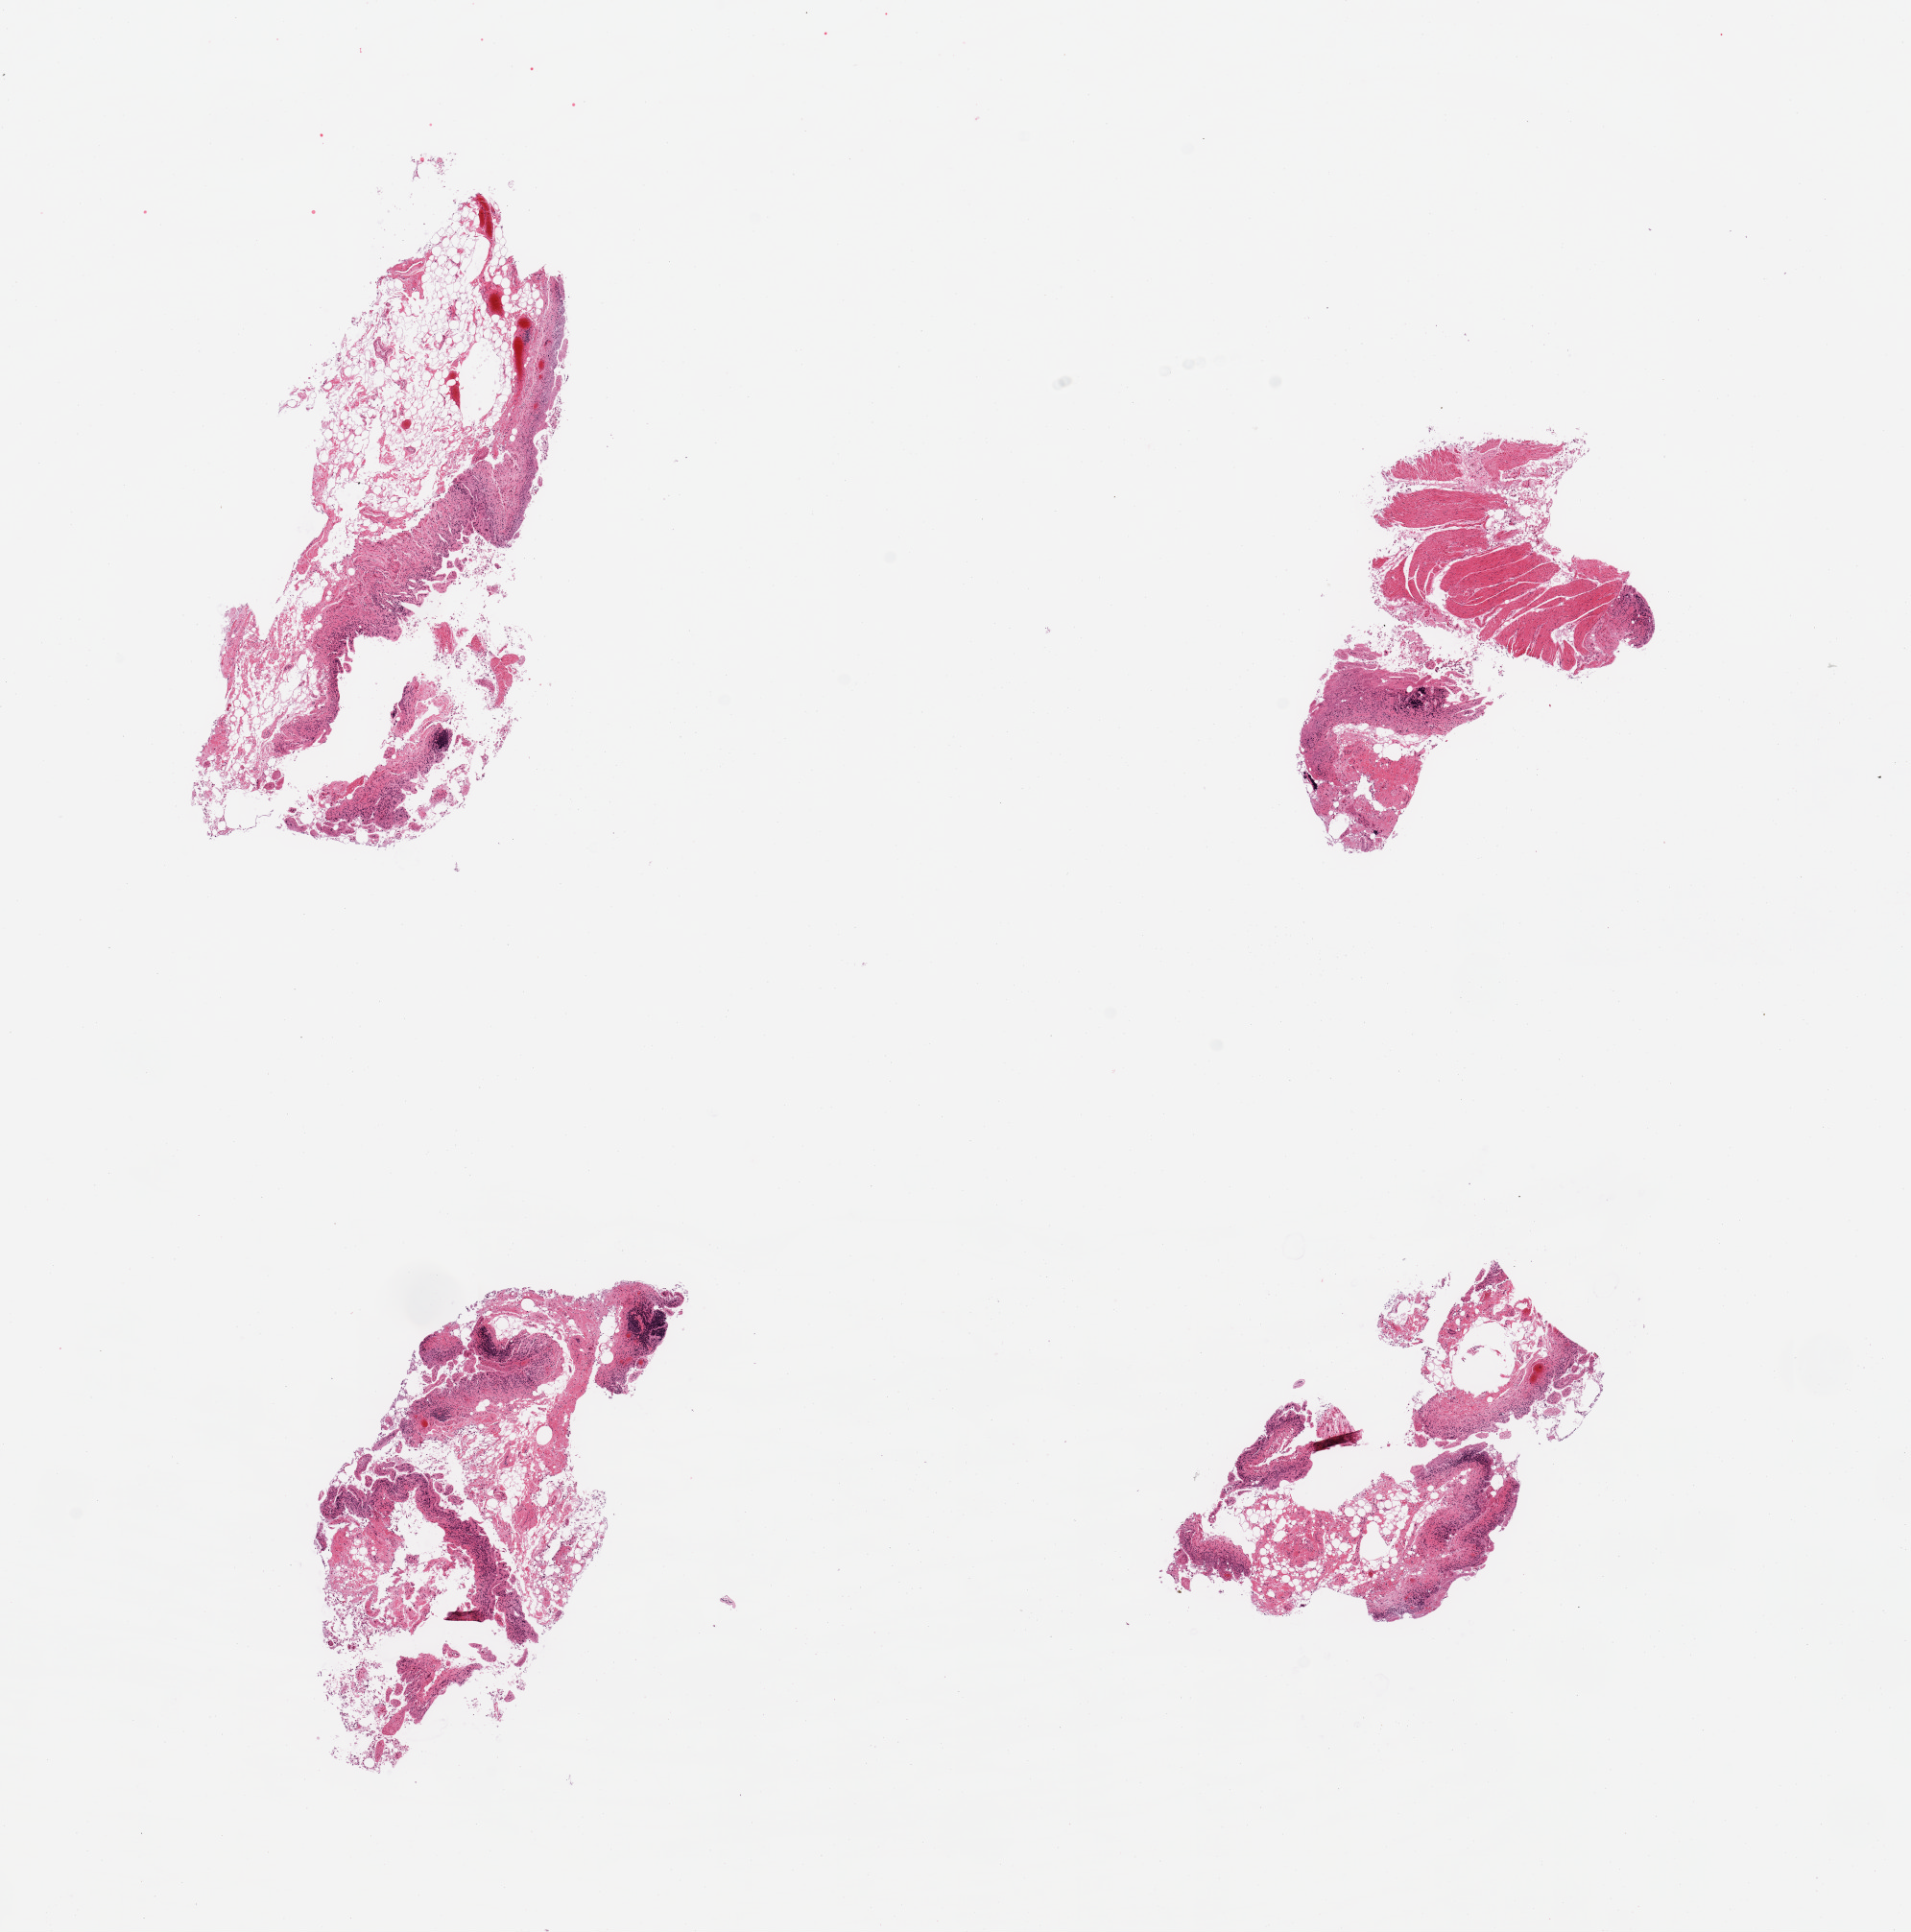
Whole-slide image, haematoxylin and eosin stain — shown as a low-resolution overview of the whole scanned area (about 15.8 x 15.9 mm, acquisition: 20x scan), PAXgene-fixed paraffin-embedded (PFPE) section, target tissue: ileum, donor tissue sample. Male donor.
Pathologist's review note for this sample: 4 pieces; inadequate lymphoid tissue.